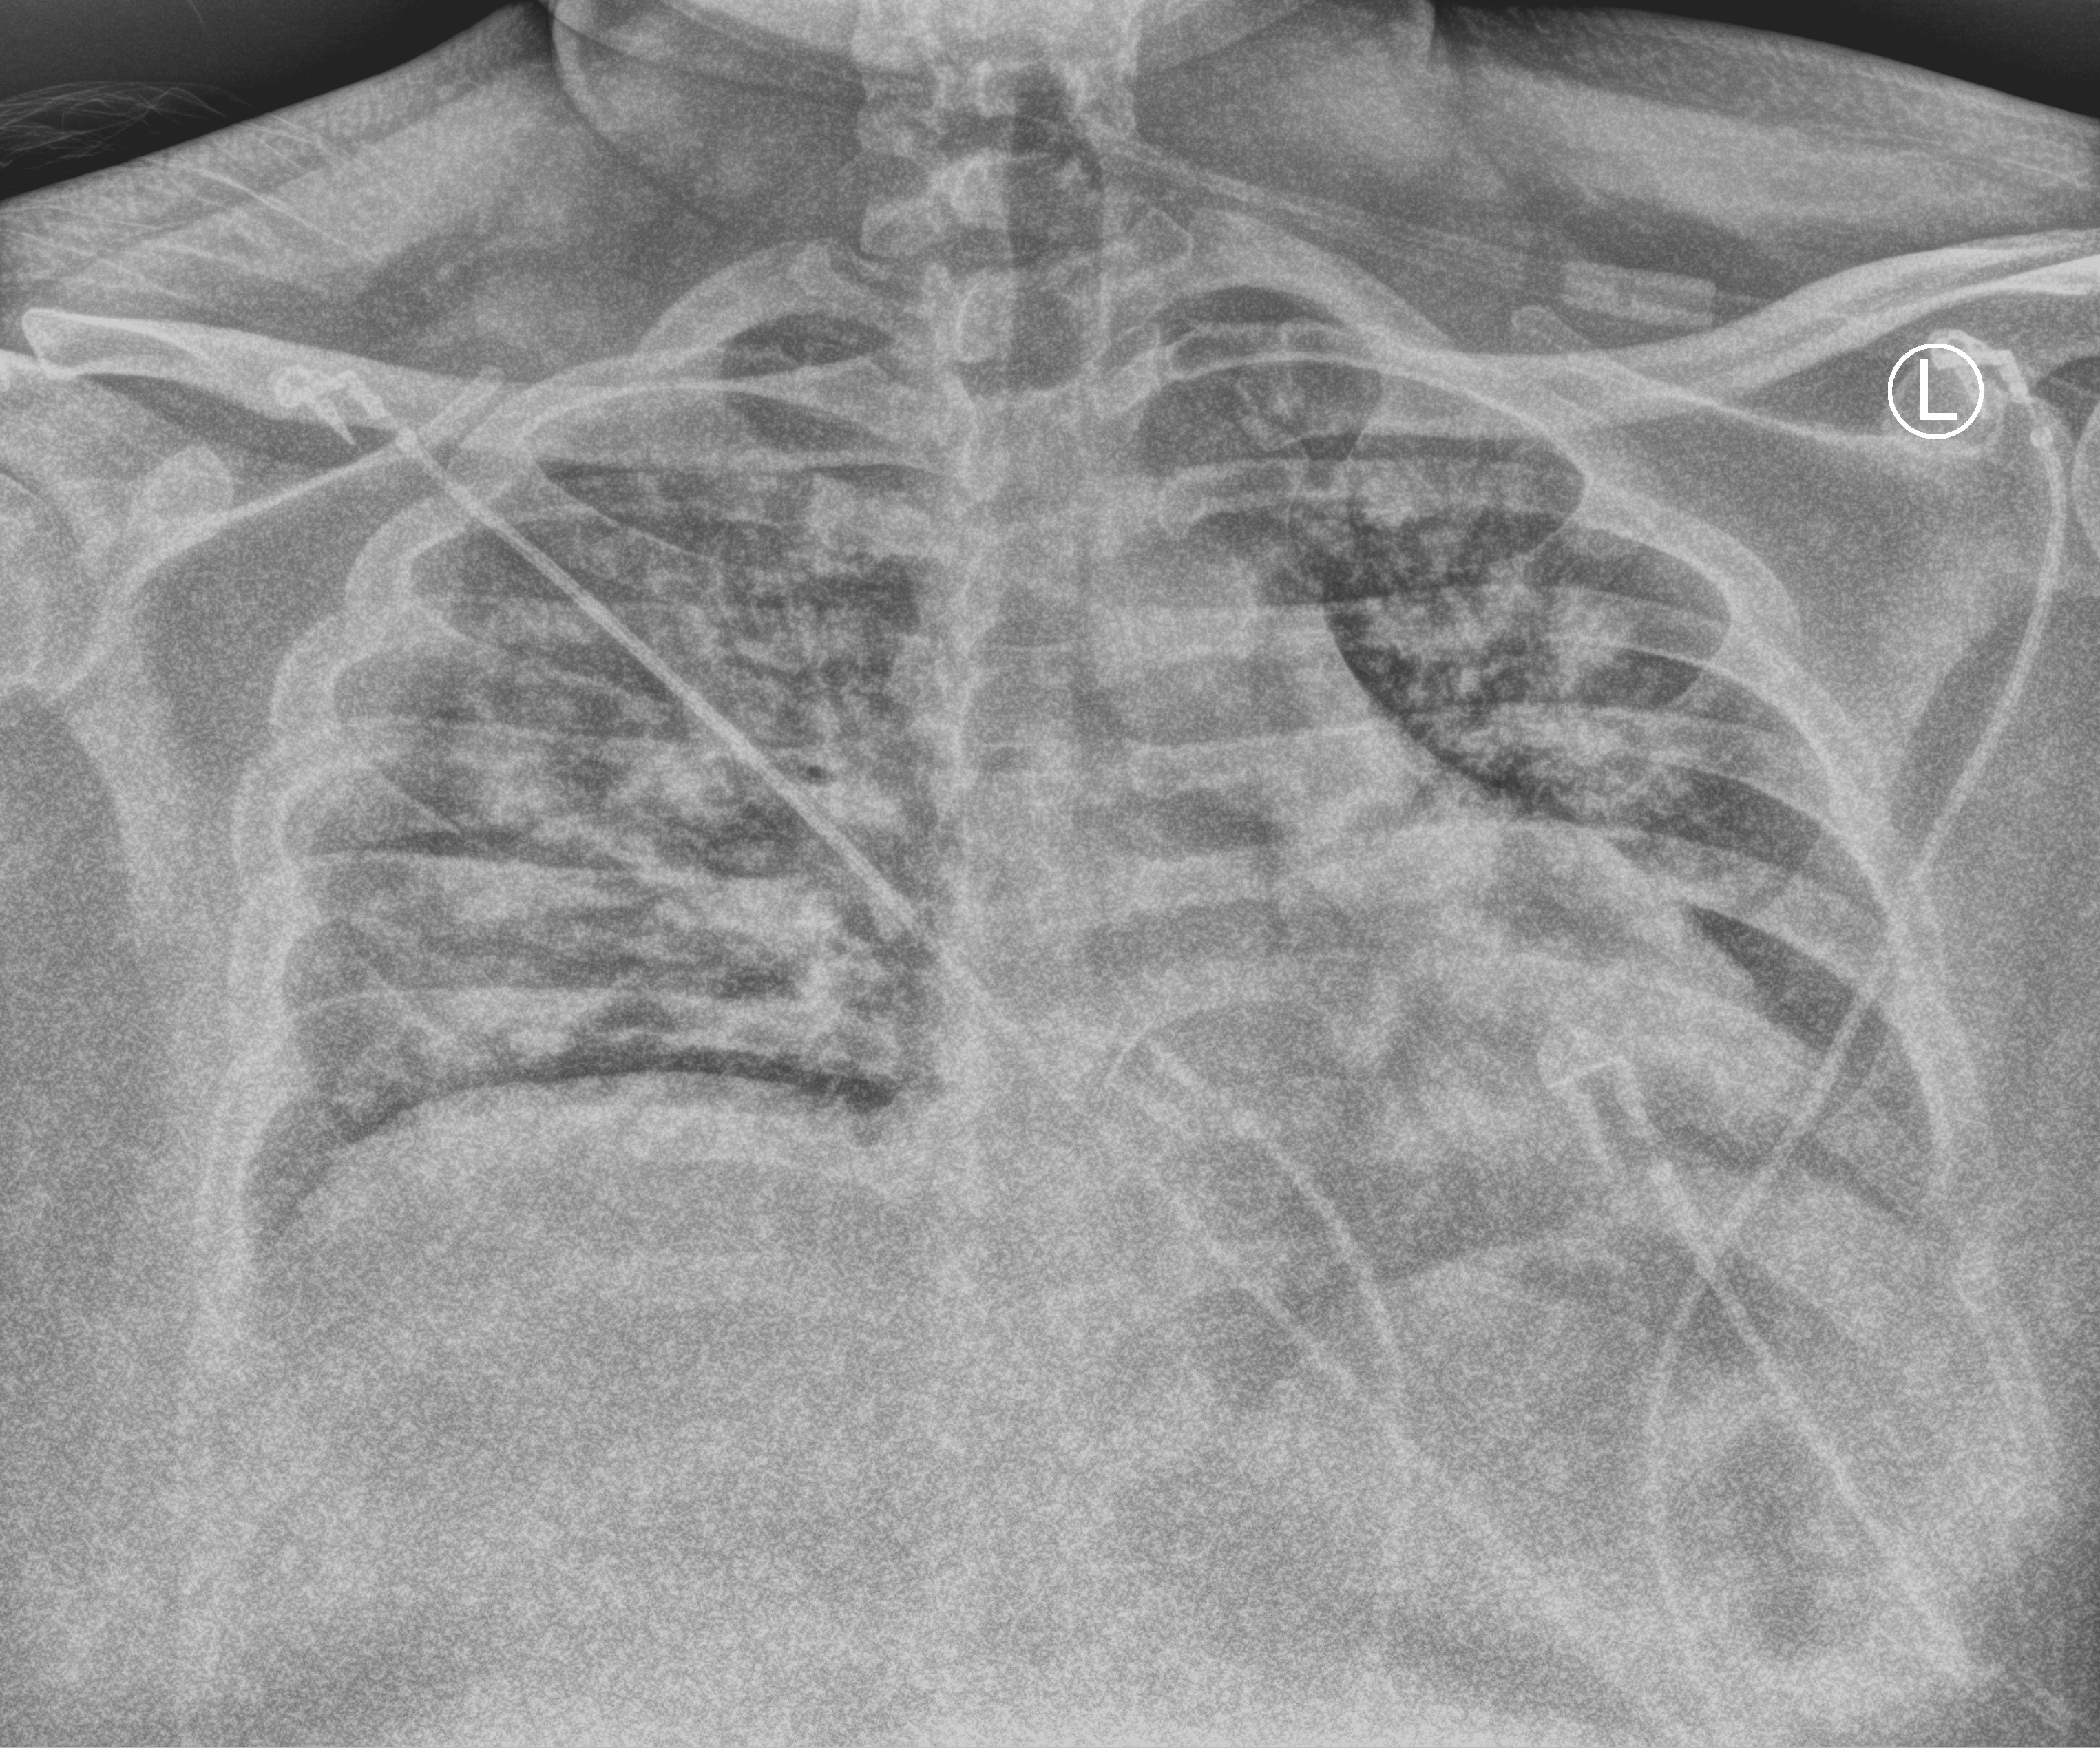
Bedside chest radiograph (computed radiography), anteroposterior (AP) projection. Male patient hospitalised with COVID-19, age 18–59 years.
From the hospital-stay record, not from the radiograph (when in the stay this image was taken is not recorded): mechanically ventilated during this hospital stay: yes.